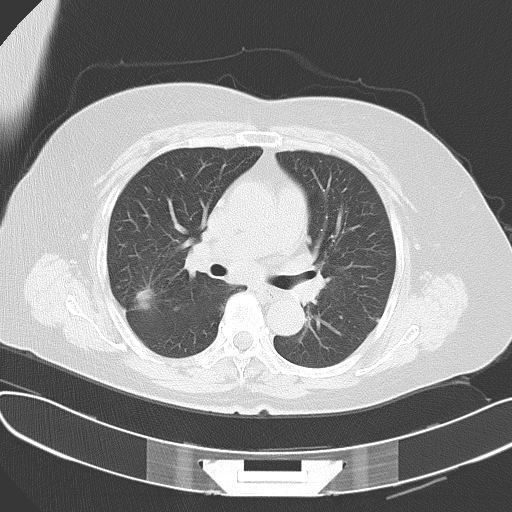
Chest CT, one axial slice. Slice 42 of 61 in the series (ordered by position). Reconstruction kernel B70f. Lung window (W 1500 / L -600 HU). 5 mm slice thickness. 512 × 512 image matrix, field of view 367 × 367 mm. Patient: female, 63 years. Case-level facts recorded for this patient, not image findings: clinical TNM (as recorded): T1c N3 M1a.
Outlined on this slice (bounding box drawn by a radiologist):
- lung tumour (recorded histology: adenocarcinoma): bounding box <129,288,163,315> (left, top, right, bottom; pixels)